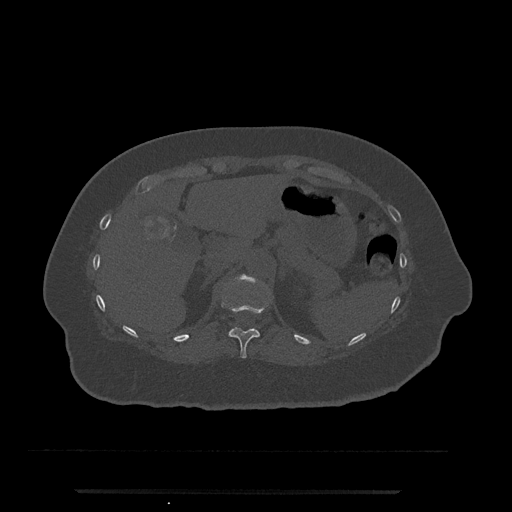
CT including the spine, one axial slice. Position 210 of 797 along the scan axis. Reconstruction kernel Br40s/3. Bone window (W 1800 / L 400 HU). 512 × 512 image matrix, field of view 440 × 440 mm. Female patient, age 51 years. Case-level facts recorded for this patient, not image findings: primary cancer: neuro; vertebrae with lytic lesions (as recorded): T8.
Annotated regions visible in this slice (semi-automatically segmented with operator editing):
- T11 vertebra: box from (x=222, y=297) to (x=269, y=359) px
- T12 vertebra: (x=242, y=275)–(x=256, y=281)